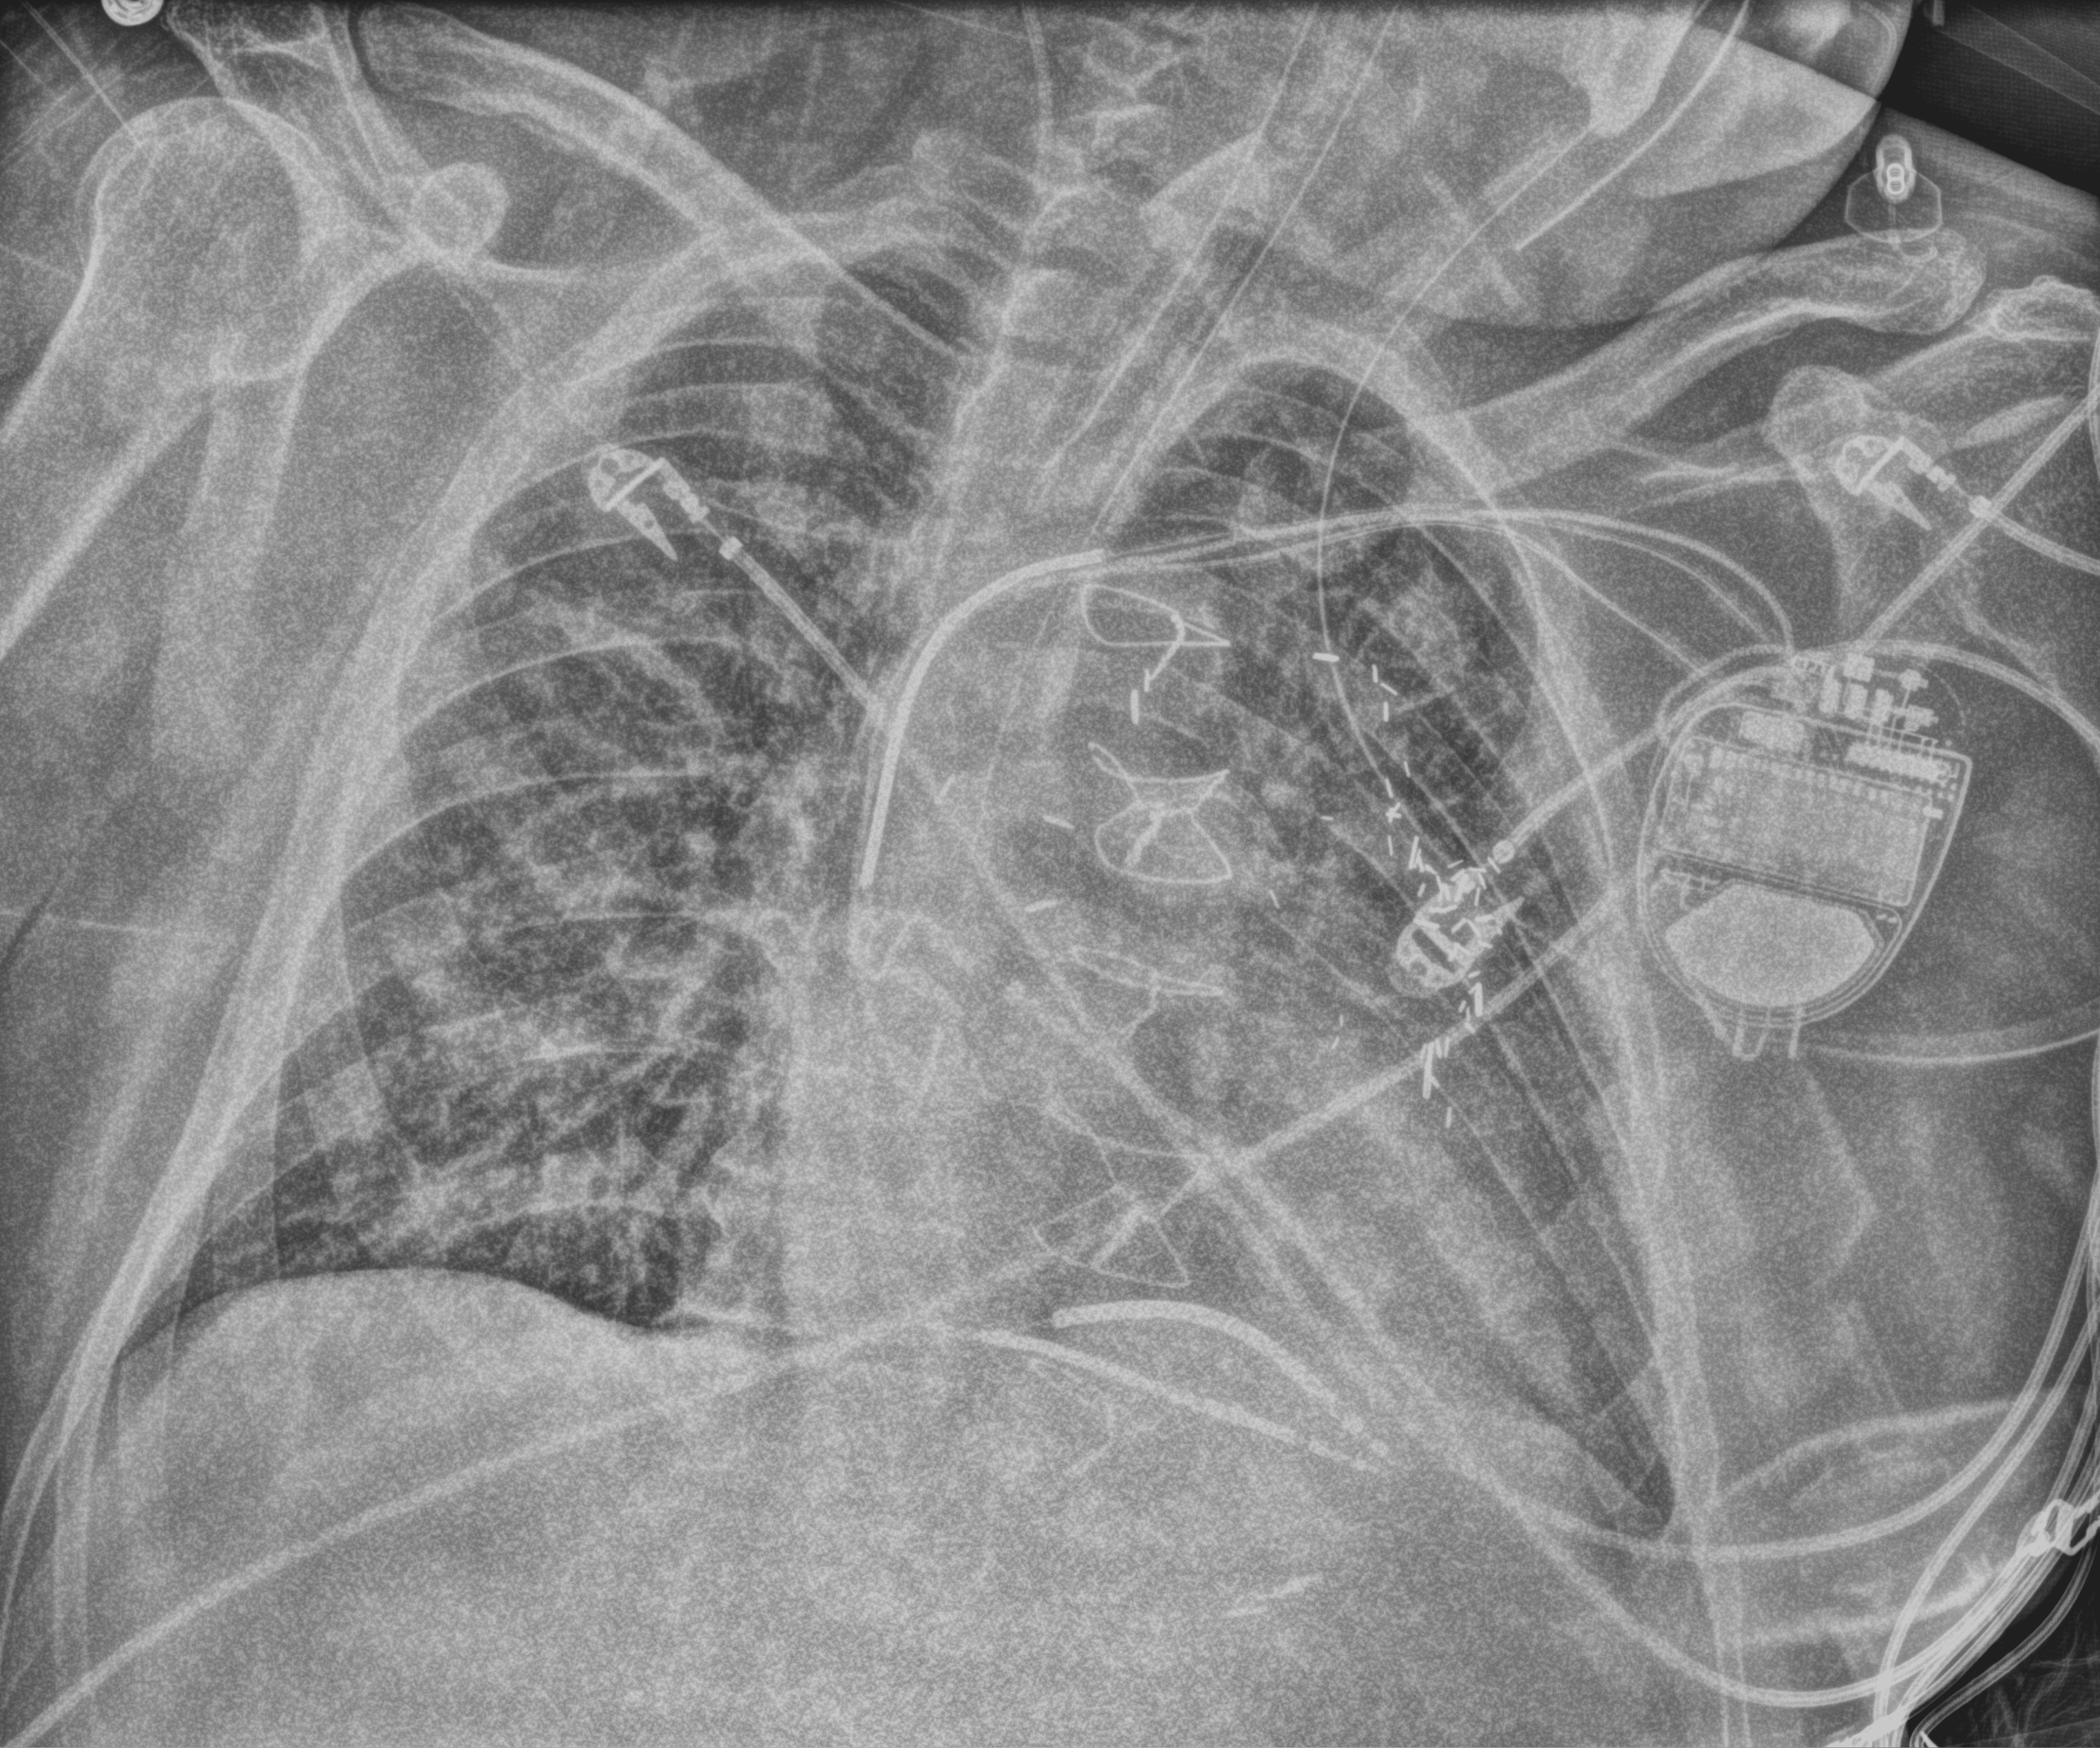
Portable chest radiograph; anteroposterior (AP) projection. Patient hospitalised with COVID-19; male, aged 60–74 years.
Hospital-stay facts (about this admission, not read from this image; timing relative to this image not recorded):
- length of hospital stay: 55 days
- admitted to intensive care during this hospital stay: yes